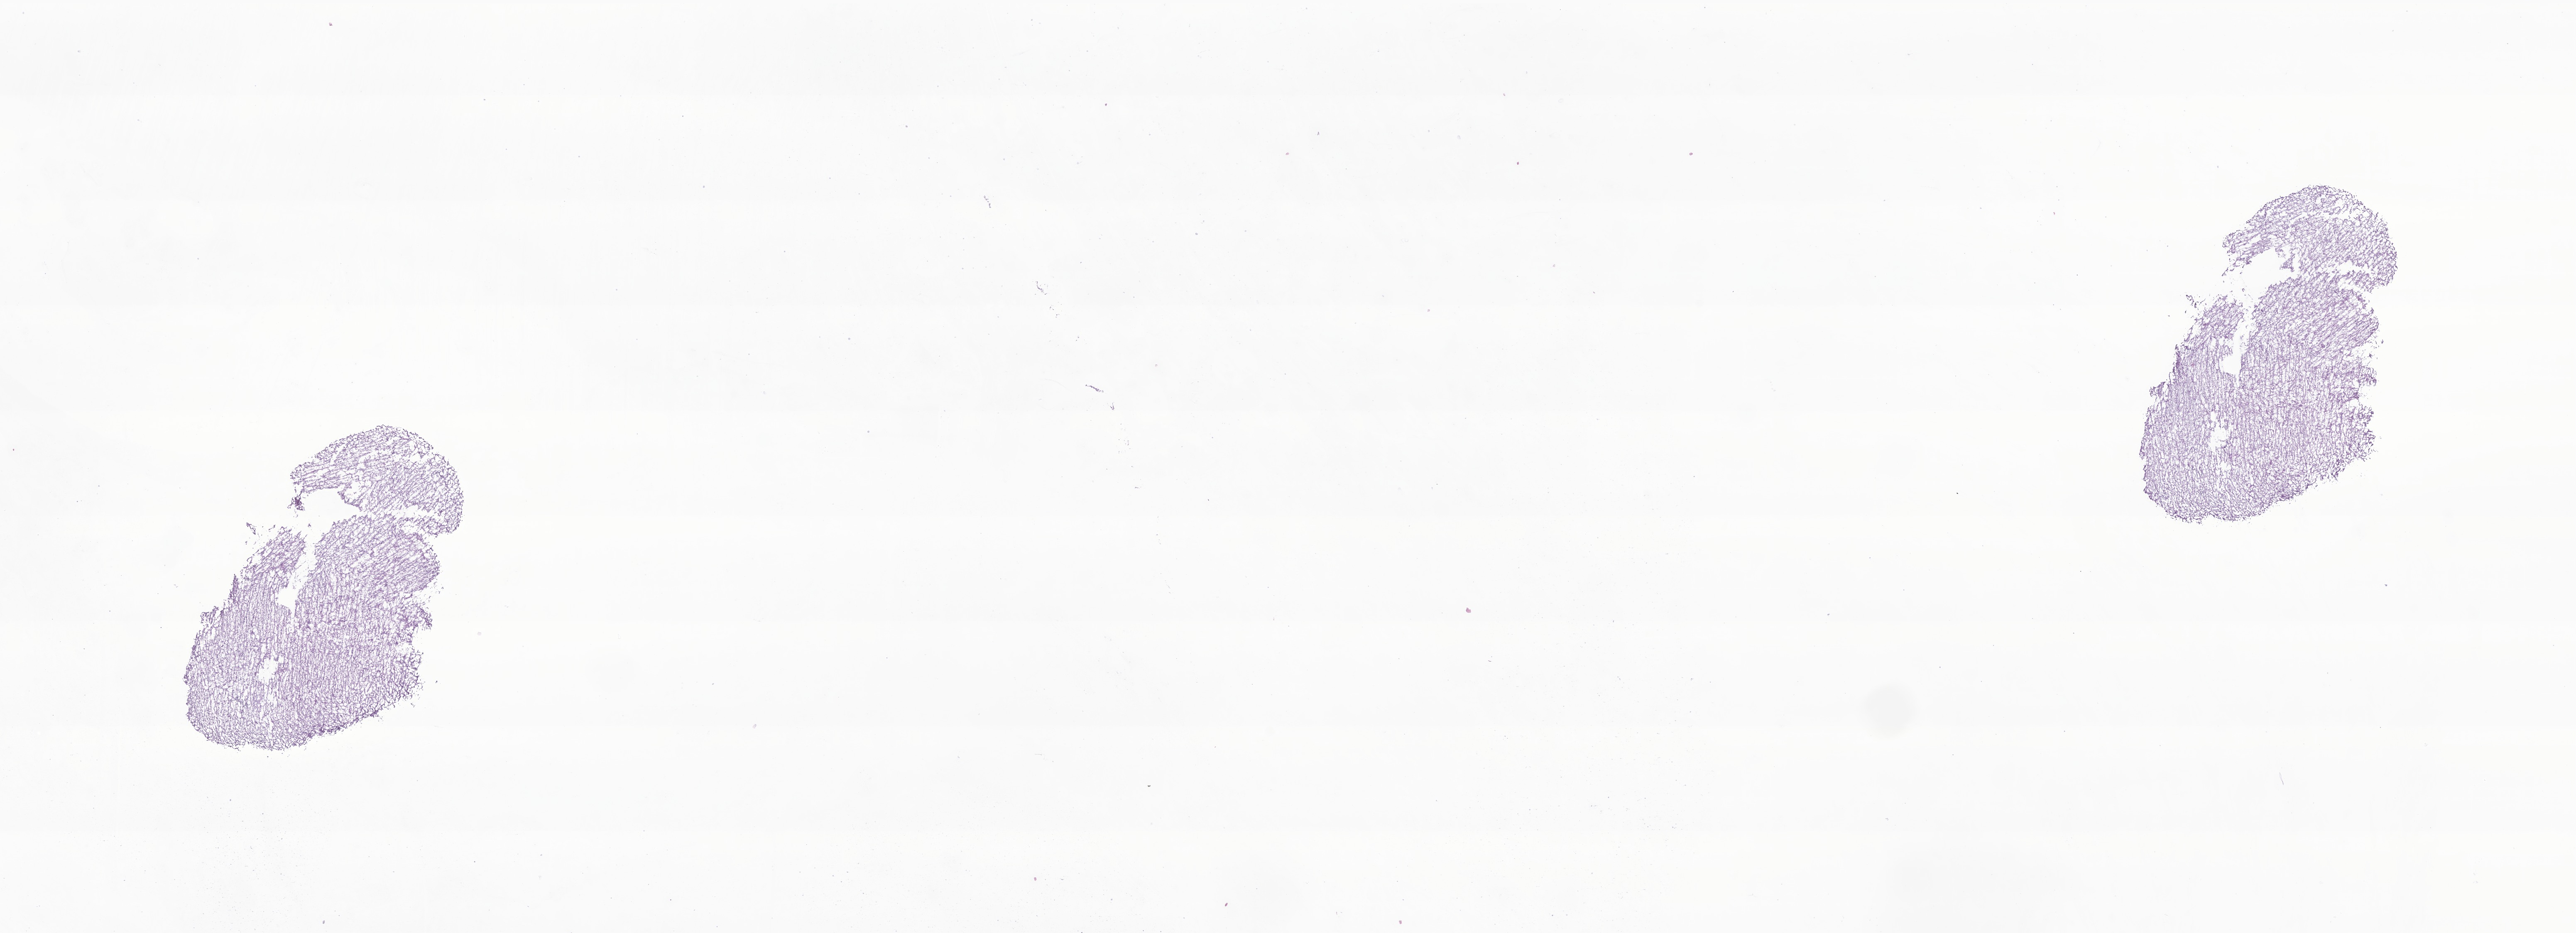
Whole-slide image, haematoxylin and eosin stain of tumor tissue from the brain — whole scanned area (about 26.2 x 9.5 mm) shown as a low-resolution overview. Cryosection (OCT / tissue freezing medium). Patient: female, age 80 months (6 years 8 months).
Recorded diagnosis: Tumor cells, uncertain whether benign or malignant.